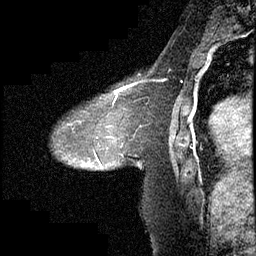
Breast MRI (dynamic contrast-enhanced), one sagittal slice. Slice 138 of 232 in the series (ordered by position). Dynamic contrast-enhanced study with each time point stored as its own series, time point 2 of 4 at this slice position (early post-contrast, ordered by acquisition time). 1.5 T. TE 4.2 ms, TR 6.7 ms. 256 × 256 image matrix, field of view 200 × 200 mm. Patient: female, 63 years. From the clinical record (not read from this slice): setting: breast cancer imaged before/during neoadjuvant chemotherapy; receptor status: triple-negative.
Annotated regions visible in this slice (semi-automatically segmented with operator editing):
- analysis volume of interest (the breast-tissue region the enhancement analysis was run in; not a lesion): bounding box (x1, y1, x2, y2) in pixels: (52, 90, 140, 171)
- tumour enhancement mask (voxels above the 70 % enhancement threshold inside the analysis volume of interest): (93, 90, 125, 165)